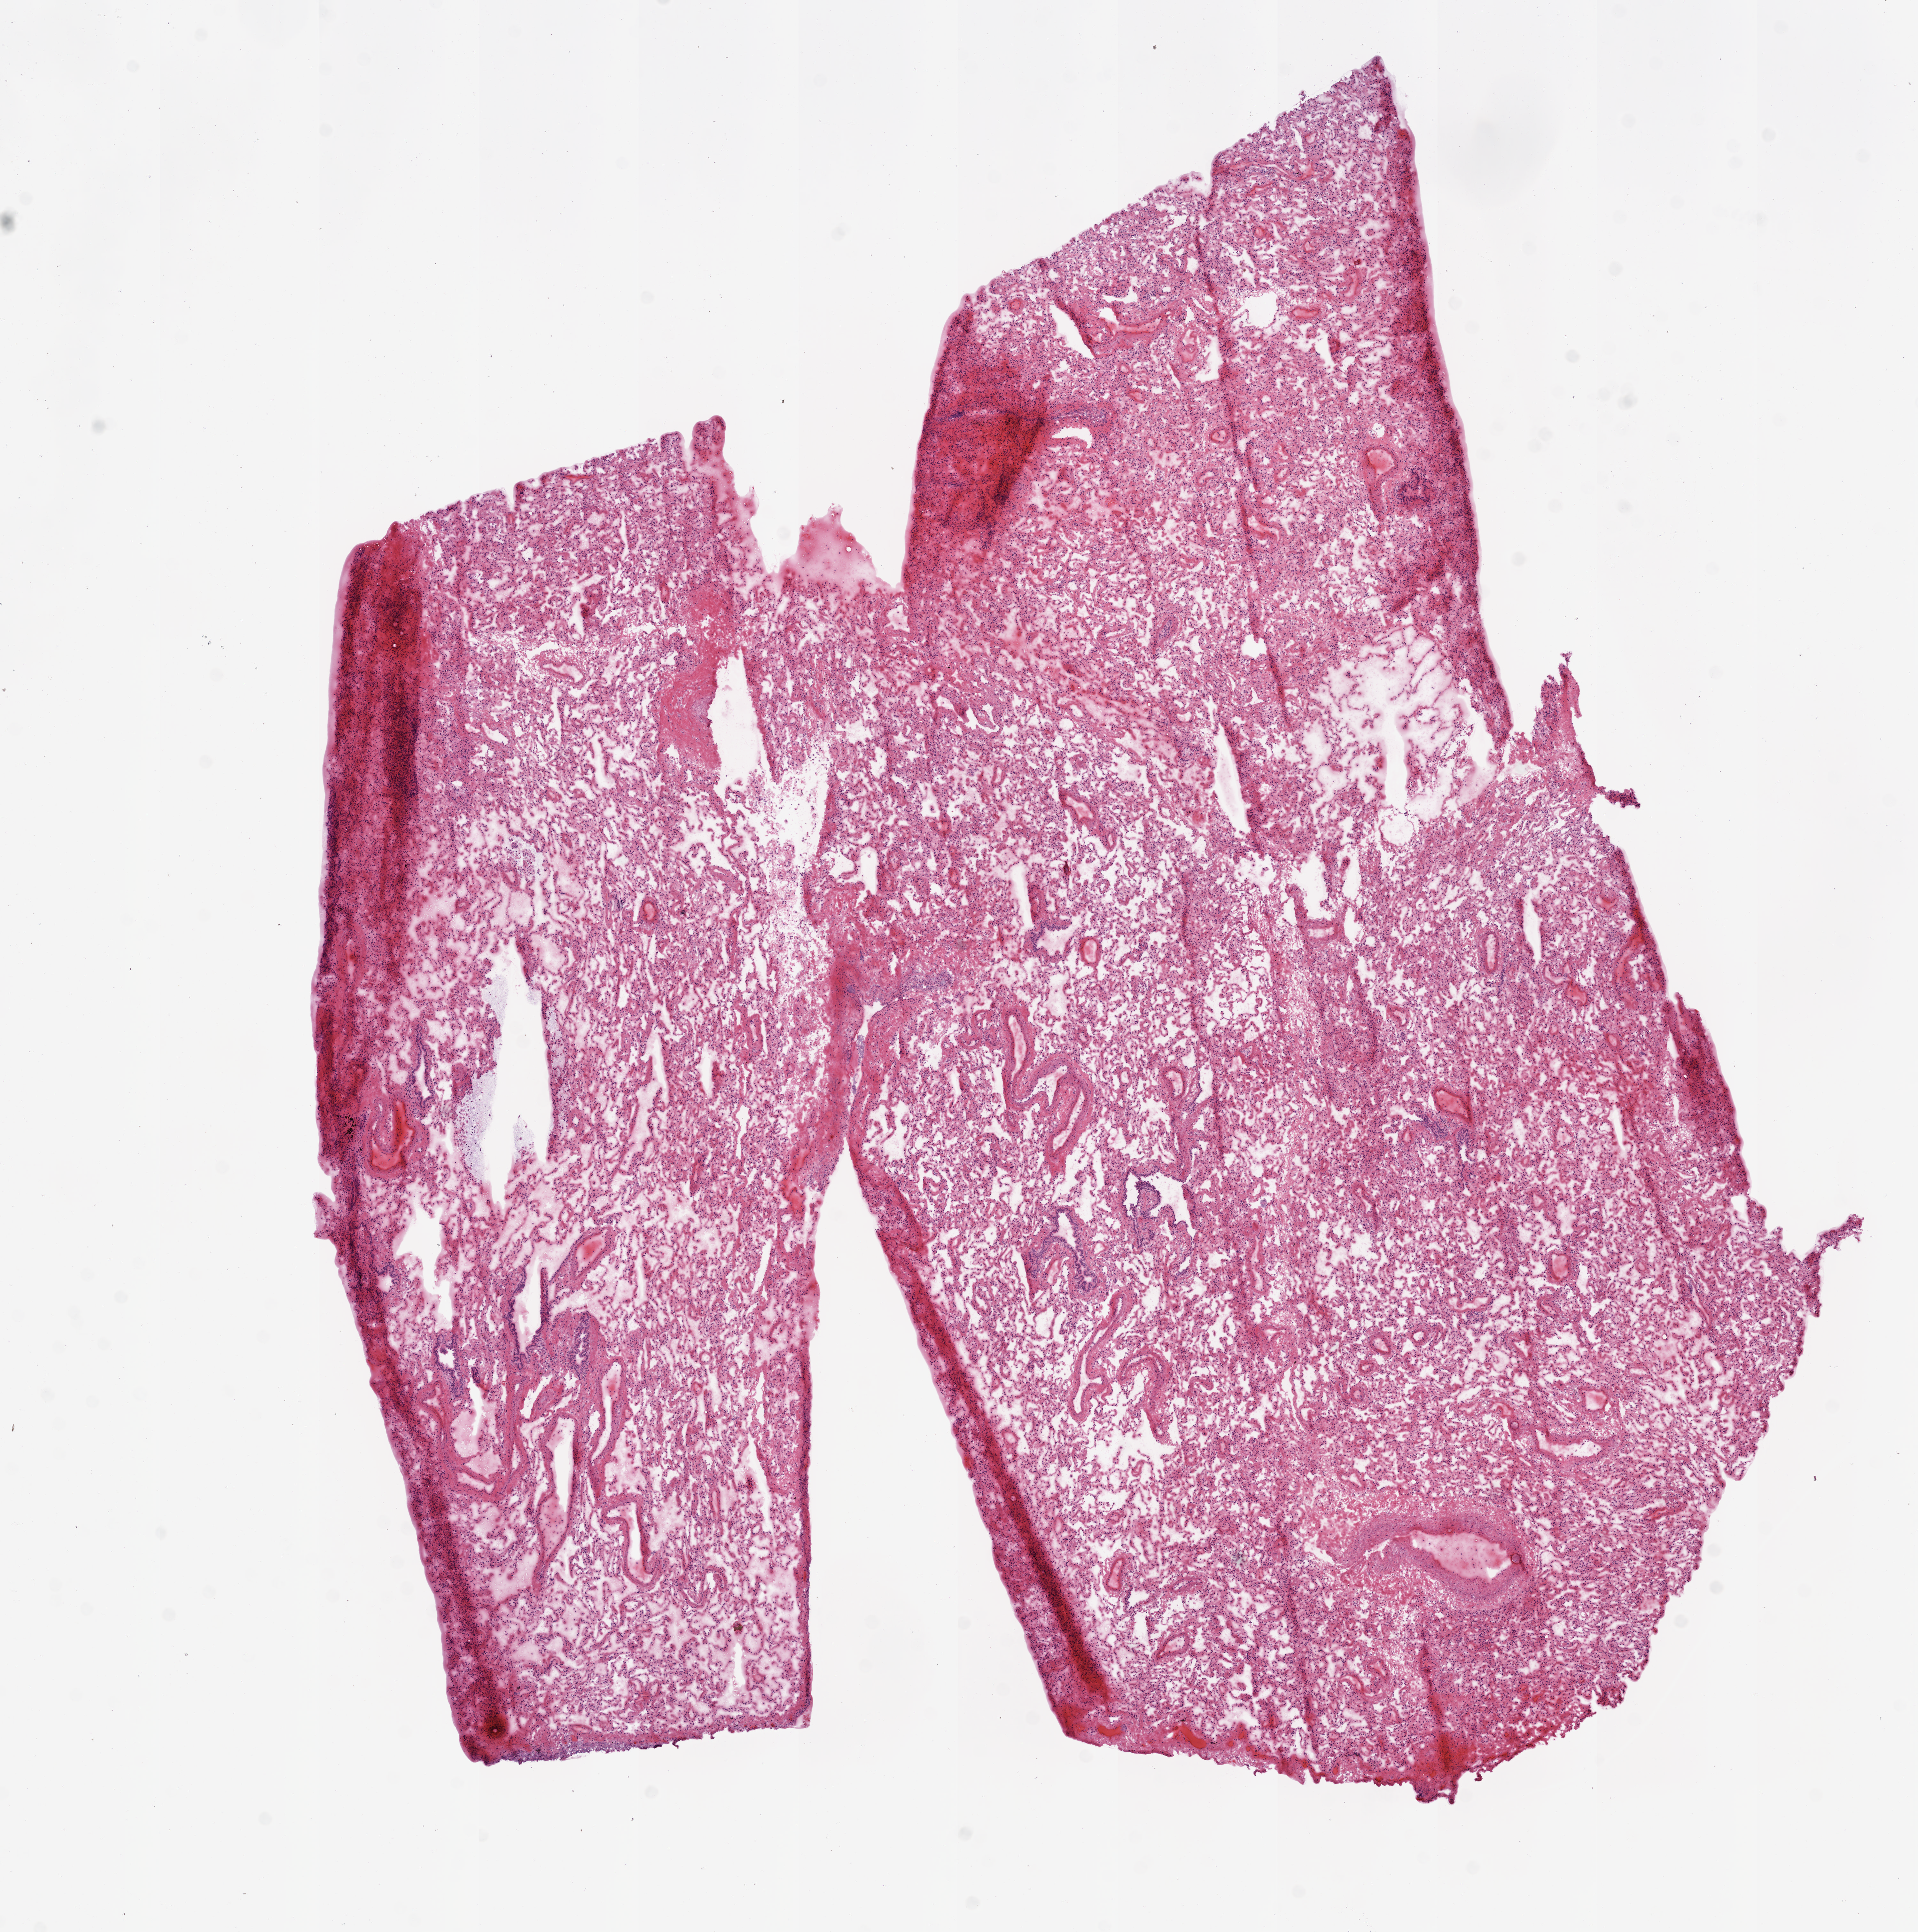
H&E-stained whole-slide image, shown as a low-resolution overview of the whole scanned area (about 12.0 x 12.1 mm, acquisition: 20x scan); frozen section from the bottom of the tissue portion; solid tissue normal (non-tumour tissue) sample from the lung. Female, age 65 years at initial diagnosis.
This section: solid tissue normal sample (biorepository sample class). Patient diagnosis: Adenocarcinoma, NOS.